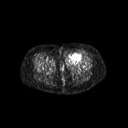
FDG PET of an extremity soft-tissue mass (from a PET/CT study), one axial slice; position 36 of 267 along the scan axis; 128 × 128 image matrix, field of view 700 × 700 mm. Female patient, age 47 years. Case-level facts recorded for this patient, not image findings: histological type: myxofibrosarcoma; grade: intermediate; site of the primary tumour: left thigh.
Outlined on this slice (expert contour drawn on MRI and transferred to this co-registered scan by the dataset authors):
- gross tumour volume including surrounding oedema: box from (x=66, y=51) to (x=83, y=65) px
- gross tumour volume (mass): (x=66, y=51)–(x=81, y=62)